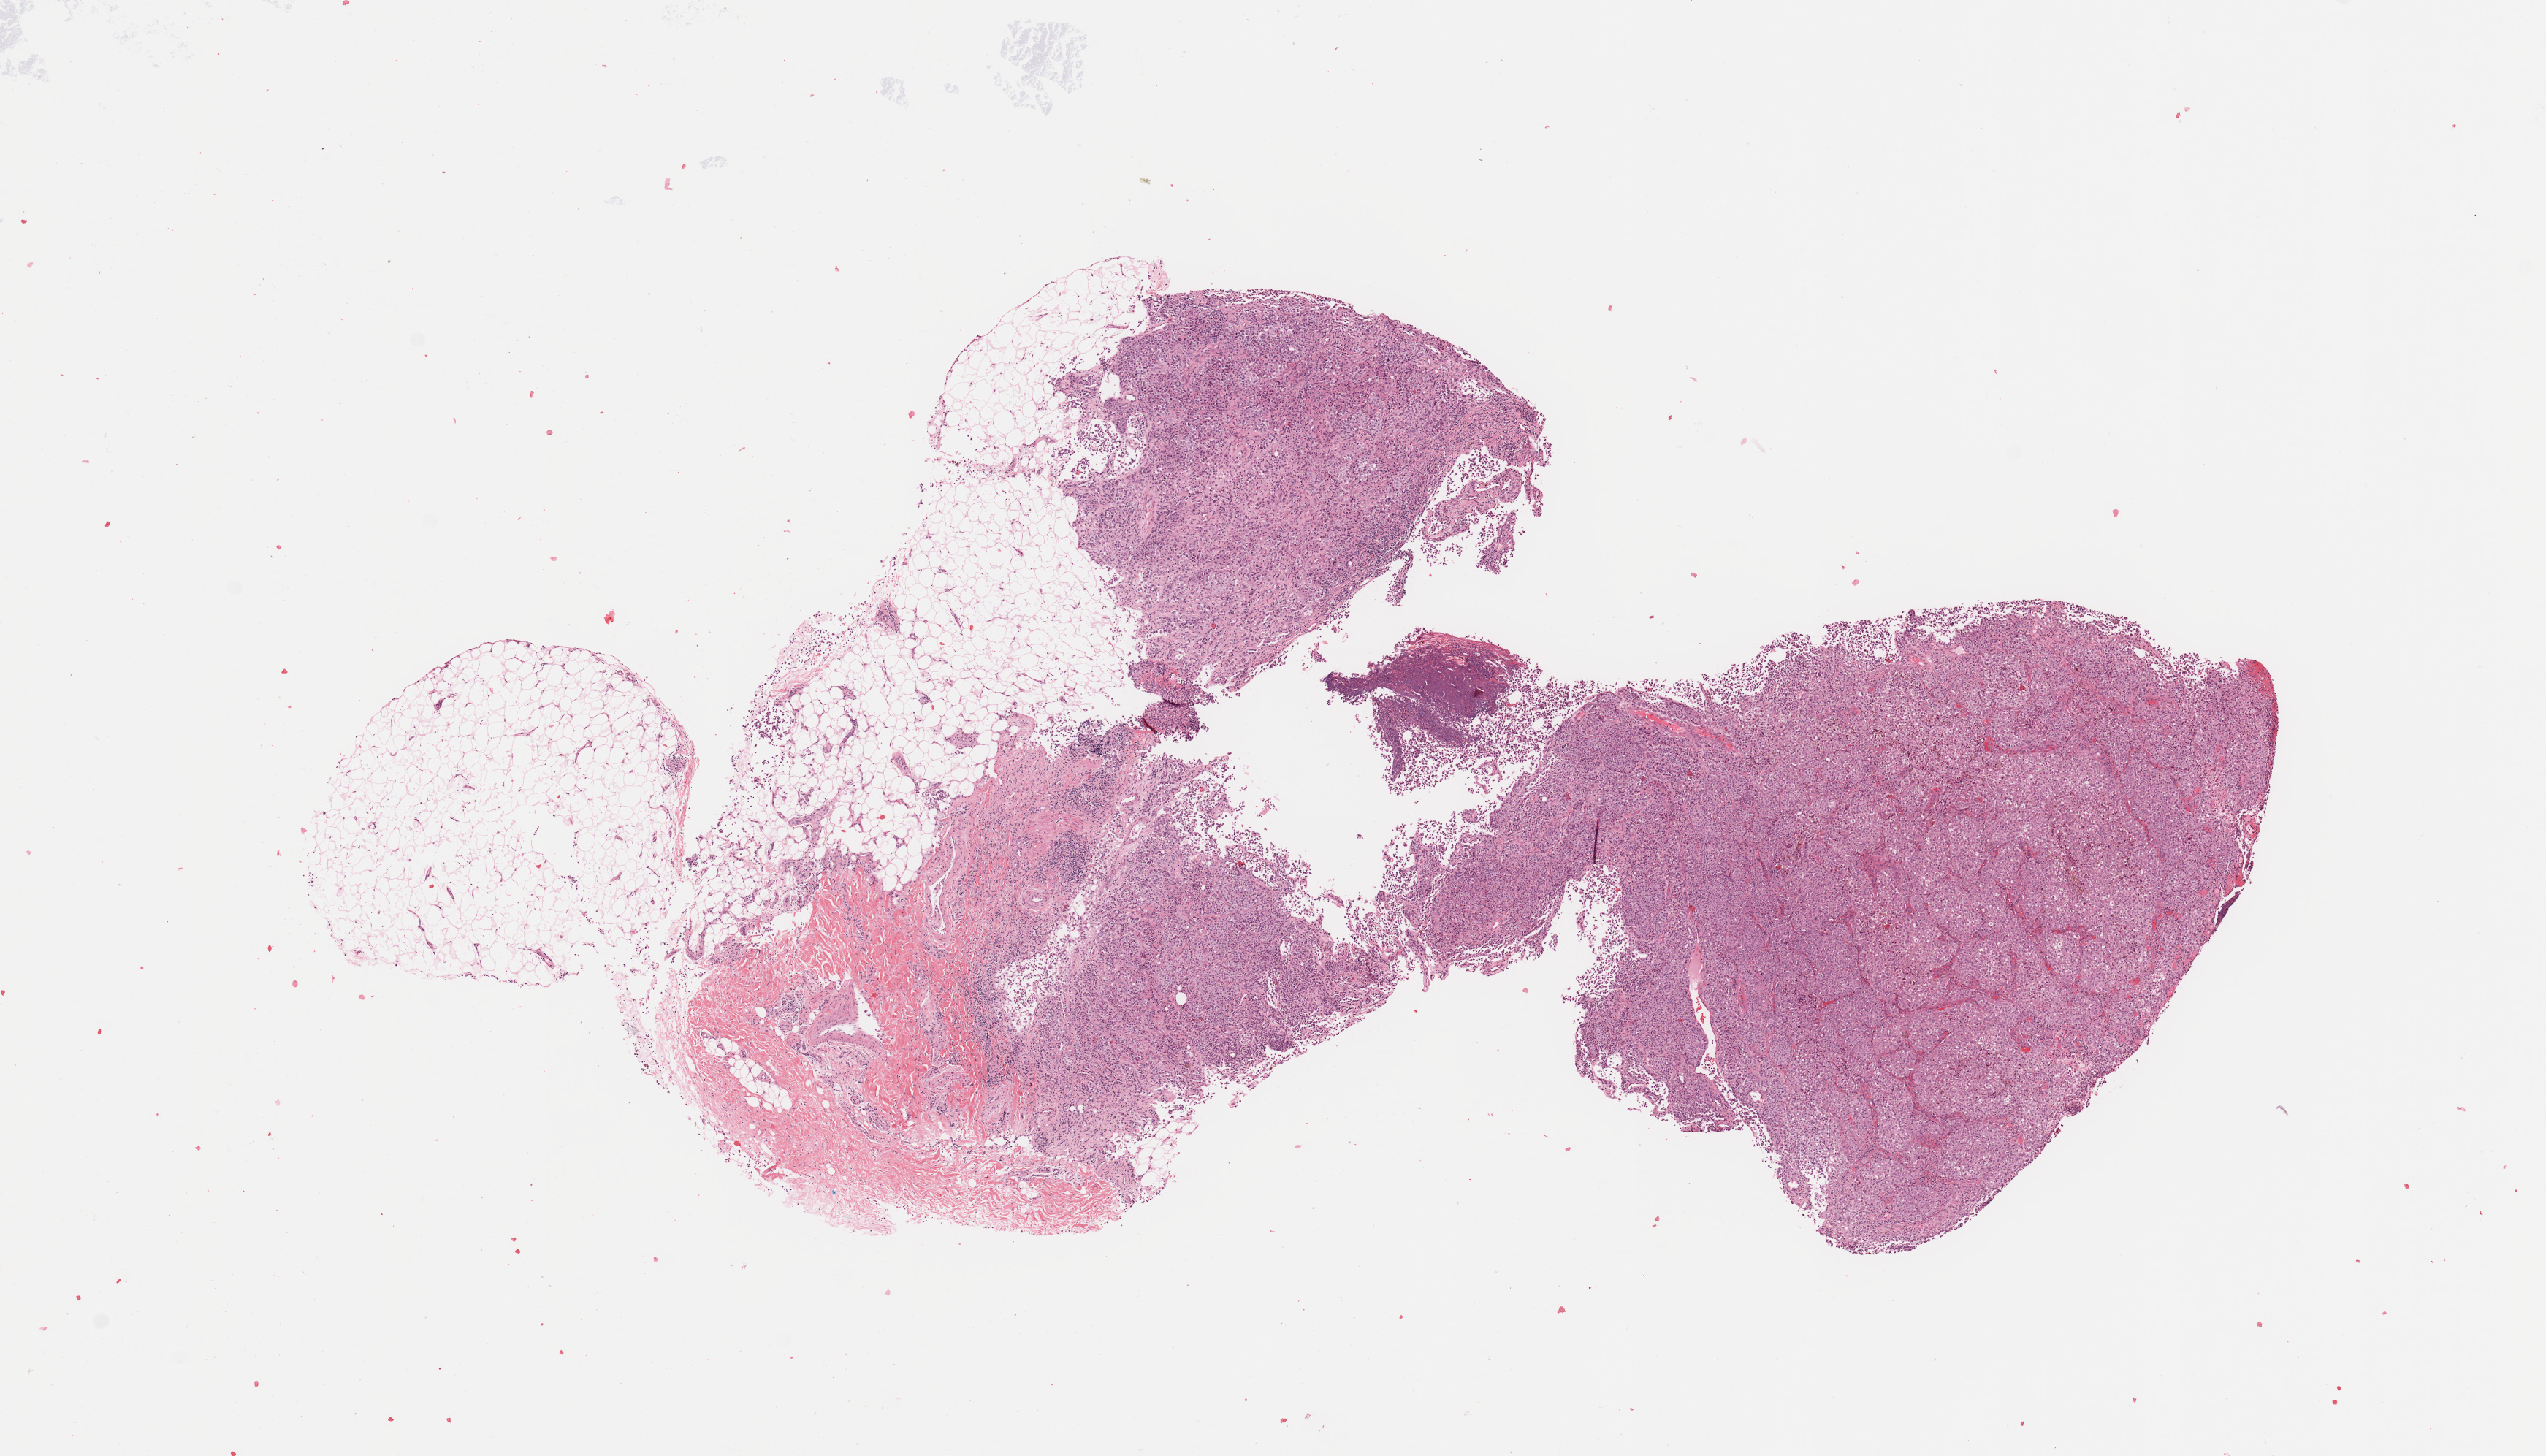
Digitized H&E-stained tissue section (whole slide) — whole scanned area (about 13.8 x 7.9 mm, acquisition: 20x scan) shown as a low-resolution overview. Tumour tissue sample, sampled site: skin. 64-year-old female patient. Composition of this section per pathologist review: tumour nuclei 80%, necrosis 0%.
• AJCC pathologic stage: IIIC
• primary tumour site (as recorded): extremities
• diagnosis: Malignant melanoma, NOS